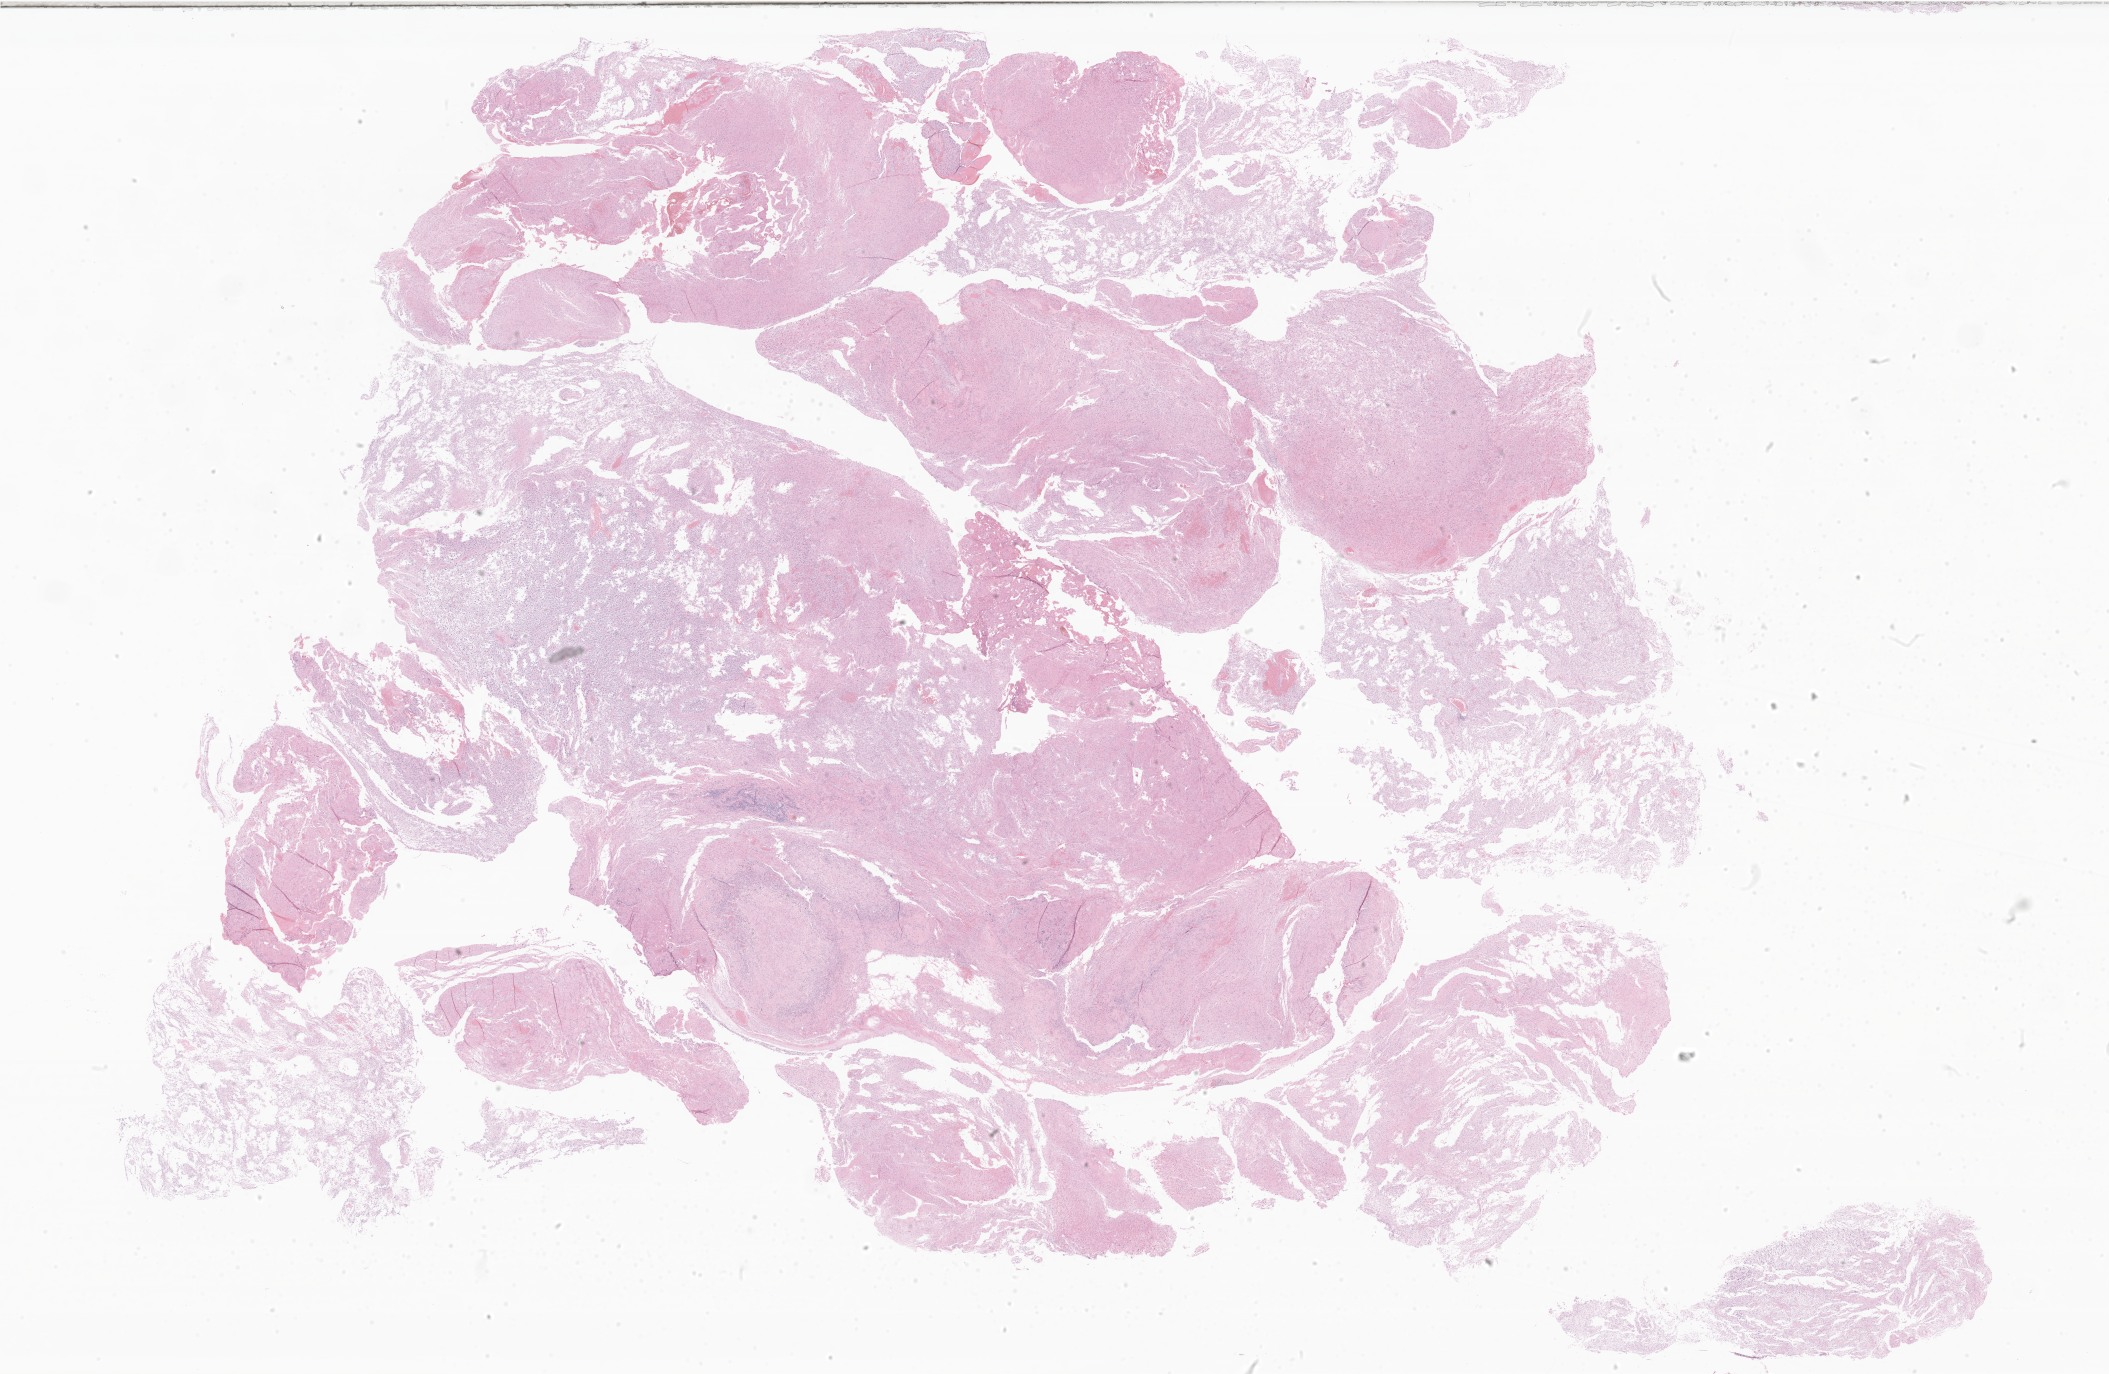
Whole-slide image, hematoxylin and eosin (H&E) stain of tumor tissue from the brain, low-resolution overview of the scanned area, about 35.6 x 23.2 mm, formalin-fixed paraffin-embedded section. Male patient, age 142 months (11 years 10 months).
Recorded diagnosis: Pilocytic astrocytoma.